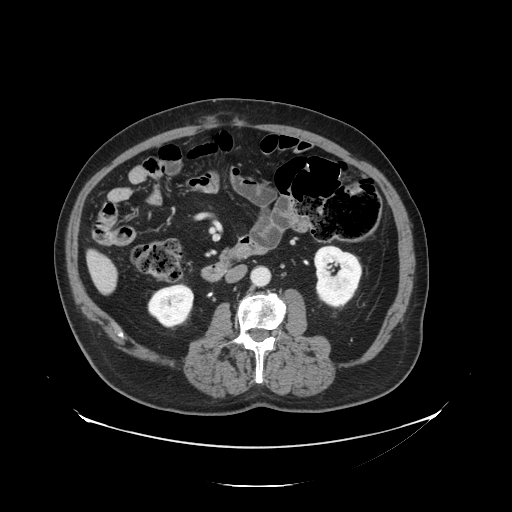
Contrast-enhanced abdominal CT, one axial slice. Slice 36 of 138 in the series (ordered by position). Reconstruction kernel STANDARD. 120 kVp. Intravenous contrast given. Soft-tissue window (W 400 / L 40 HU). 512 × 512 image matrix. Male patient, age 77 years. From the clinical record (not read from this slice): diagnosis: colorectal cancer liver metastases, imaged before liver resection; multiple liver metastases: no; largest metastasis: 1.5 cm.
Structures marked on this image (expert manual segmentation):
- liver: box from (x=90, y=253) to (x=117, y=293) px
- planned liver remnant (the part of the liver to remain after resection): (x=89, y=252)–(x=113, y=275)